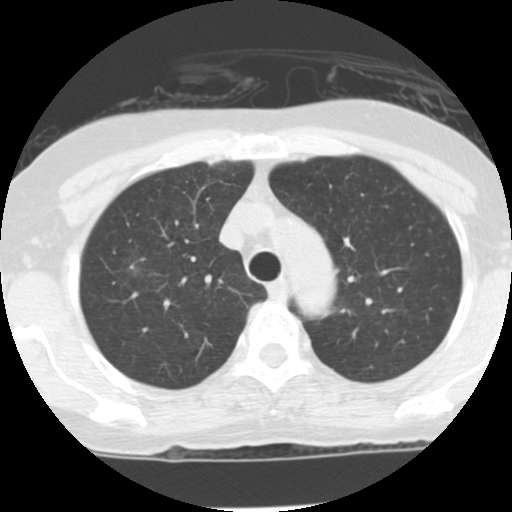
Axial slice from a low-dose chest CT screening exam, third screening round (two years after baseline), lung window (W 1500 / L -600 HU), 2.5 mm slice thickness, slice 27 of 122 in the series, 512 × 512 image matrix, field of view 290 × 290 mm. Female participant, aged 62 years at enrolment.
- Lesion marked by an expert reader, box from (x=106, y=242) to (x=160, y=293) px.
- Reader record for this screening exam (exam-level; its link to the box is not recorded): non-calcified nodule or mass ≥4 mm, right upper lobe, 9 × 8 mm, poorly defined margins, ground glass attenuation, pre-existing on the prior screen: yes; interval growth: yes.
- Later outcome: lung cancer diagnosed 134 days after this screen — bronchiolo-alveolar adenocarcinoma, NOS, right upper lobe, stage IA (AJCC 6th edition), 10 mm at pathology.